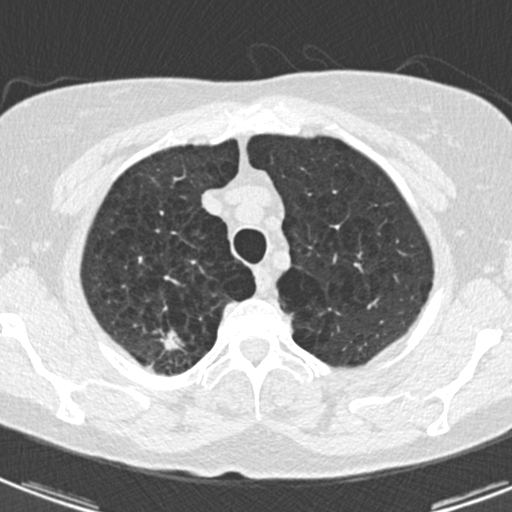
Low-dose screening chest CT, axial slice. Third annual screen. Lung window (W 1500 / L -600 HU). 2 mm slice thickness. Standard (soft-tissue) reconstruction kernel (B30f). Slice 26 of 174 in the series. Female, age 59 years at enrolment. Current smoker at enrolment.
Expert reader's lesion annotation, box from (x=134, y=320) to (x=195, y=367) px. Reader record for this screening exam (exam-level; its link to the box is not recorded): non-calcified nodule or mass ≥4 mm, right upper lobe, 12 × 7 mm, spiculated (stellate) margins, soft tissue attenuation, pre-existing on the prior screen: yes; interval growth: yes. Official screen result: positive, other. Later outcome: lung cancer diagnosed 32 days after this screen — adenocarcinoma, NOS, right upper lobe, poorly differentiated (G3), stage IA (AJCC 6th edition), 20 mm at pathology.